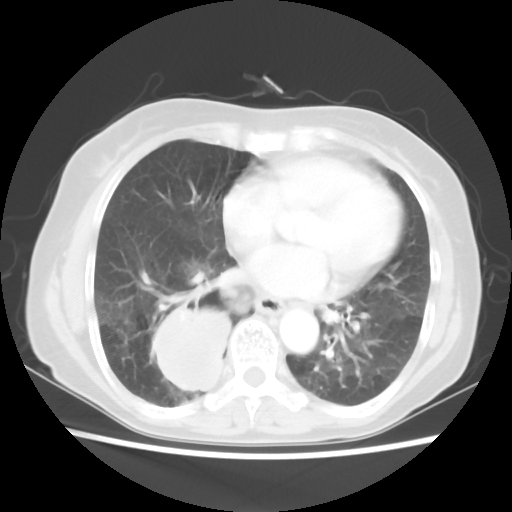
Chest CT, one axial slice; position 25 of 56 along the scan axis; reconstruction kernel STANDARD; lung window (W 1500 / L -600 HU); 5 mm slice thickness; 512 × 512 image matrix, field of view 332 × 332 mm. Female patient, age 66 years. Case-level facts recorded for this patient, not image findings: clinical TNM (as recorded): T2 N3 M0.
Outlined on this slice (bounding box drawn by a radiologist):
- lung tumour (recorded histology: small cell carcinoma): box from (x=145, y=309) to (x=245, y=401) px